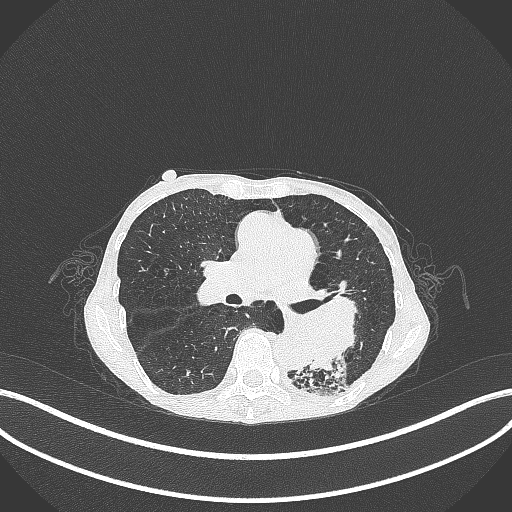
Chest CT, one axial slice. Slice 151 of 347 in the series (ordered by position). 120 kVp. Lung window (W 1500 / L -600 HU). 1 mm slice thickness. 512 × 512 image matrix, field of view 400 × 400 mm. Patient: female, 70 years. From the clinical record (not read from this slice): clinical TNM (as recorded): T3 N0 M0; histopathological grade: G3.
Outlined on this slice (rectangle marked by the reading radiologist):
- lung tumour (recorded histology: small cell carcinoma): bounding box (x1, y1, x2, y2) in pixels: (262, 293, 365, 378)